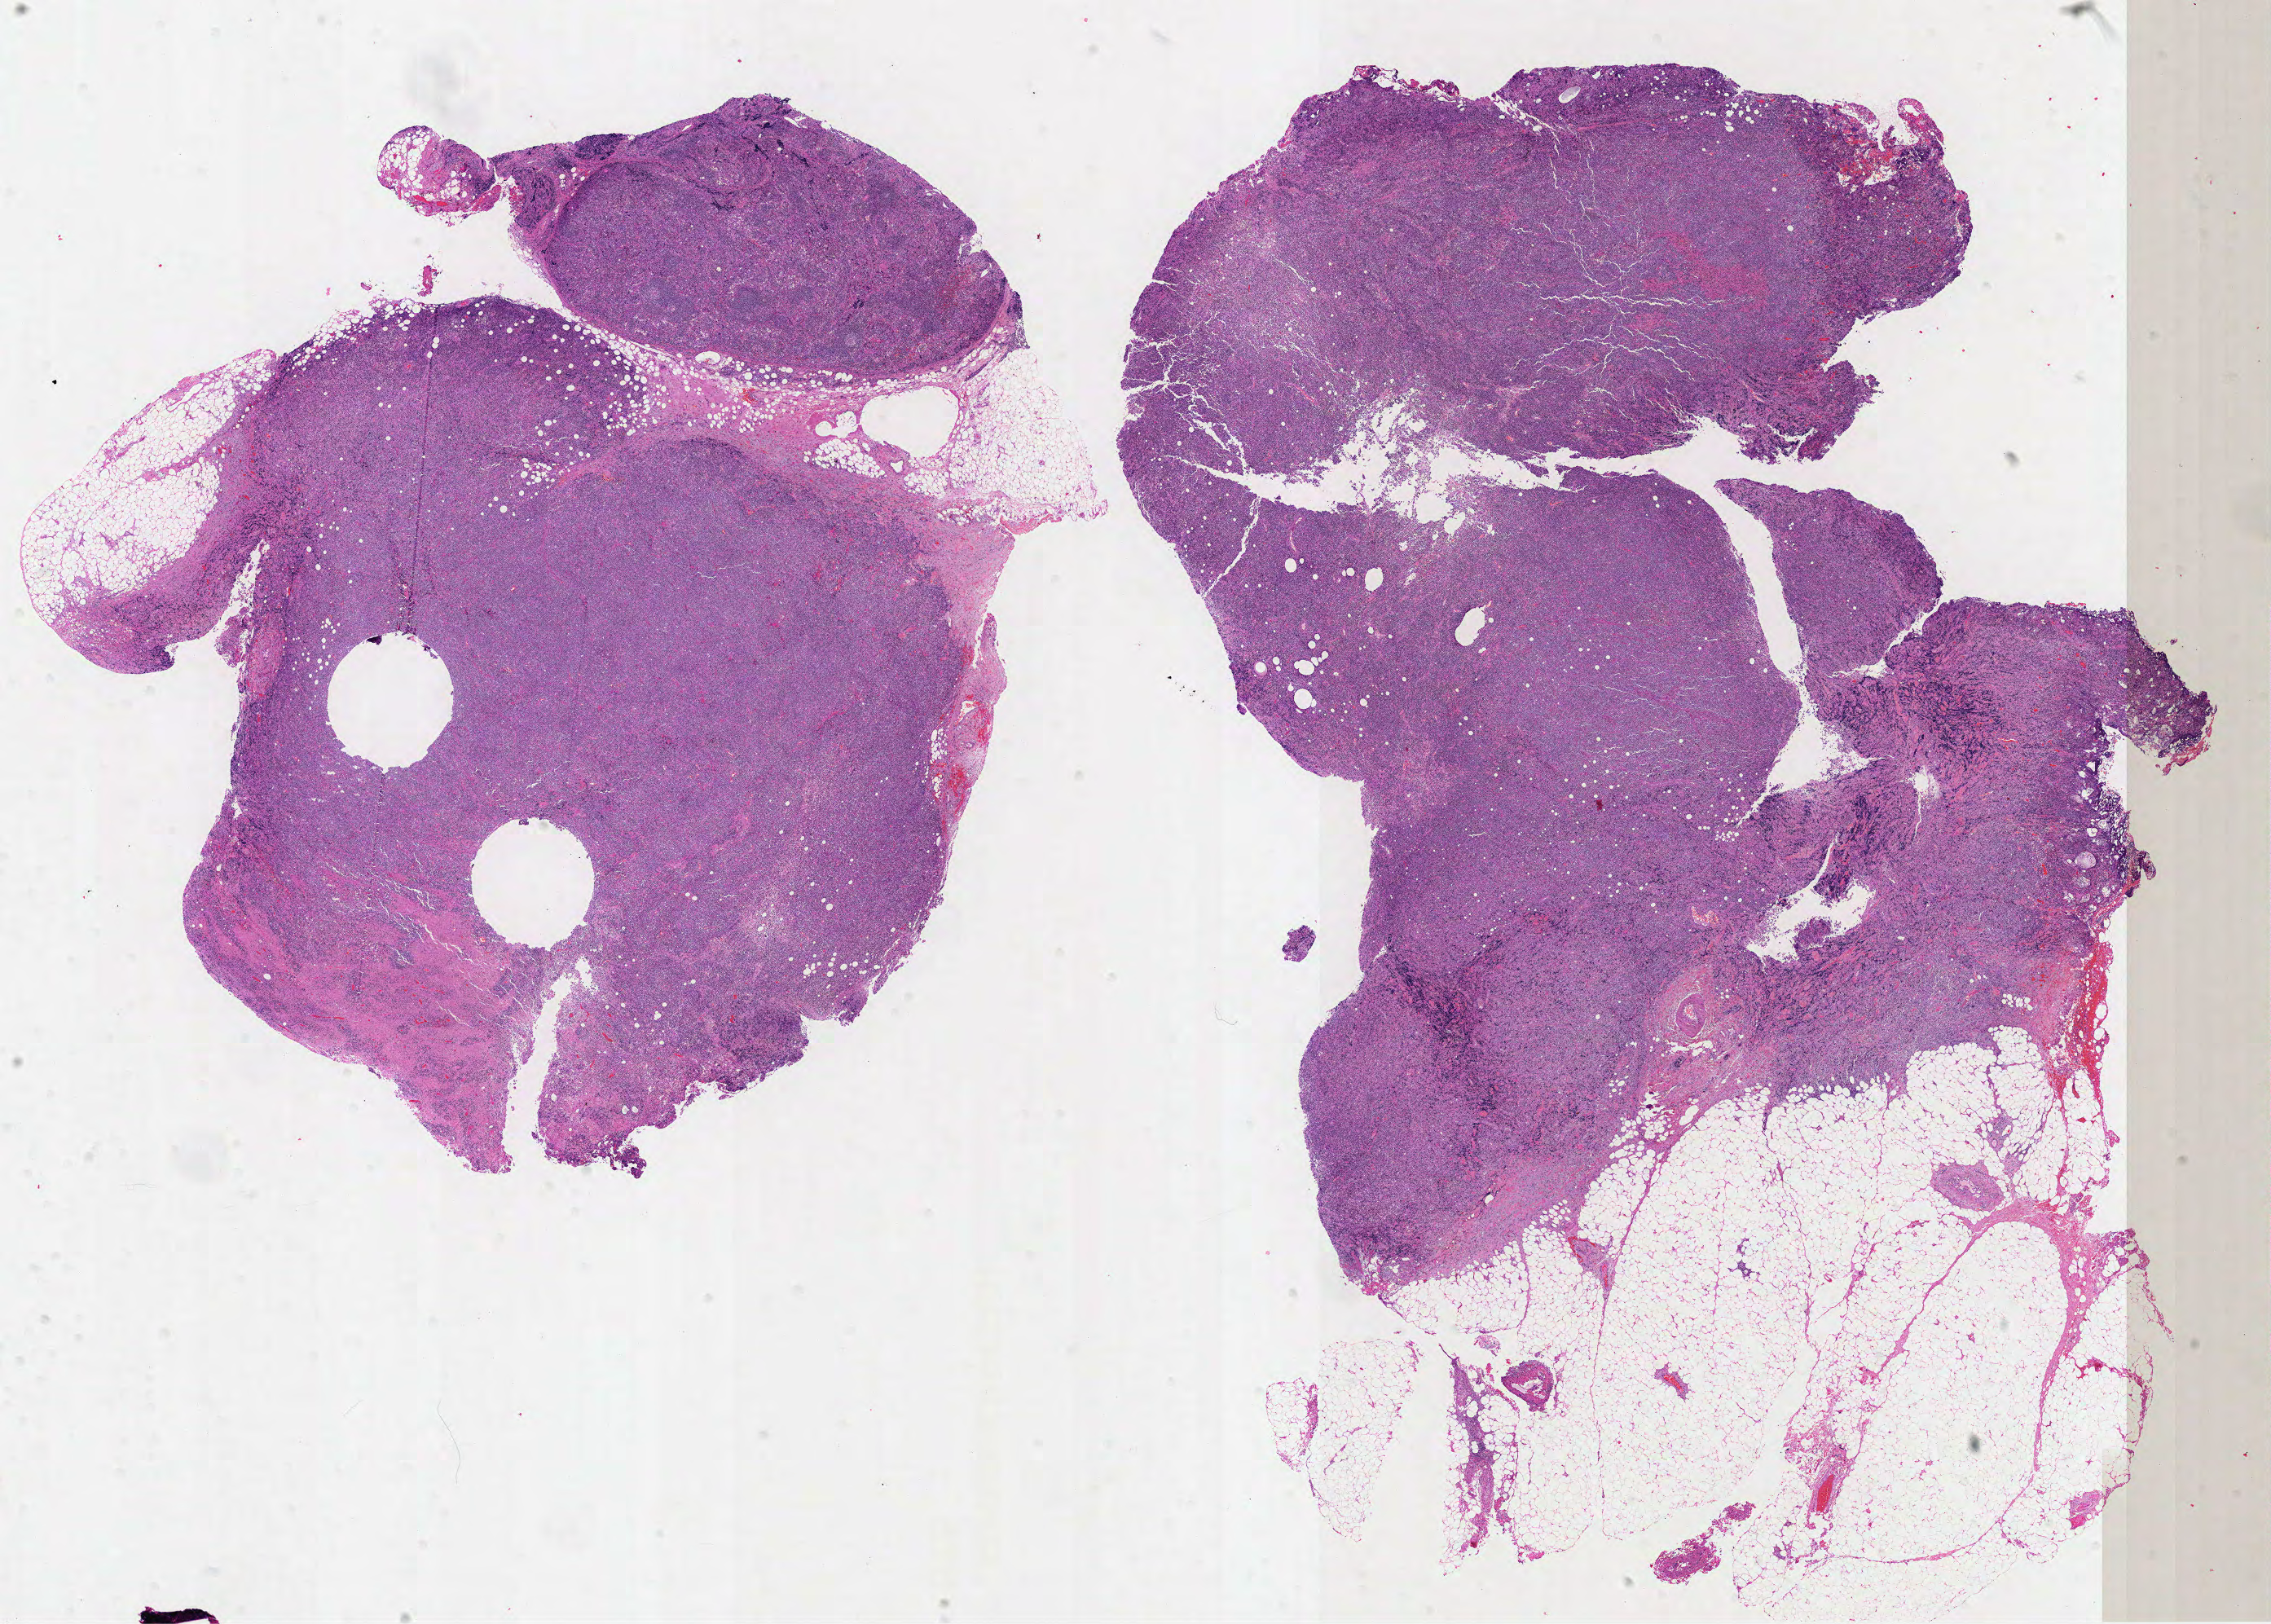
Digitized H&E-stained tissue section (whole slide), low-resolution overview of the scanned area, about 22.5 x 16.1 mm (from a 40x scan); formalin-fixed paraffin-embedded (FFPE) diagnostic section; lymphoid tissue, primary tumour sample. Female, age 57 years at initial diagnosis.
Pathologic diagnosis: Diffuse large B-cell lymphoma, NOS (lymph nodes of head, face and neck).